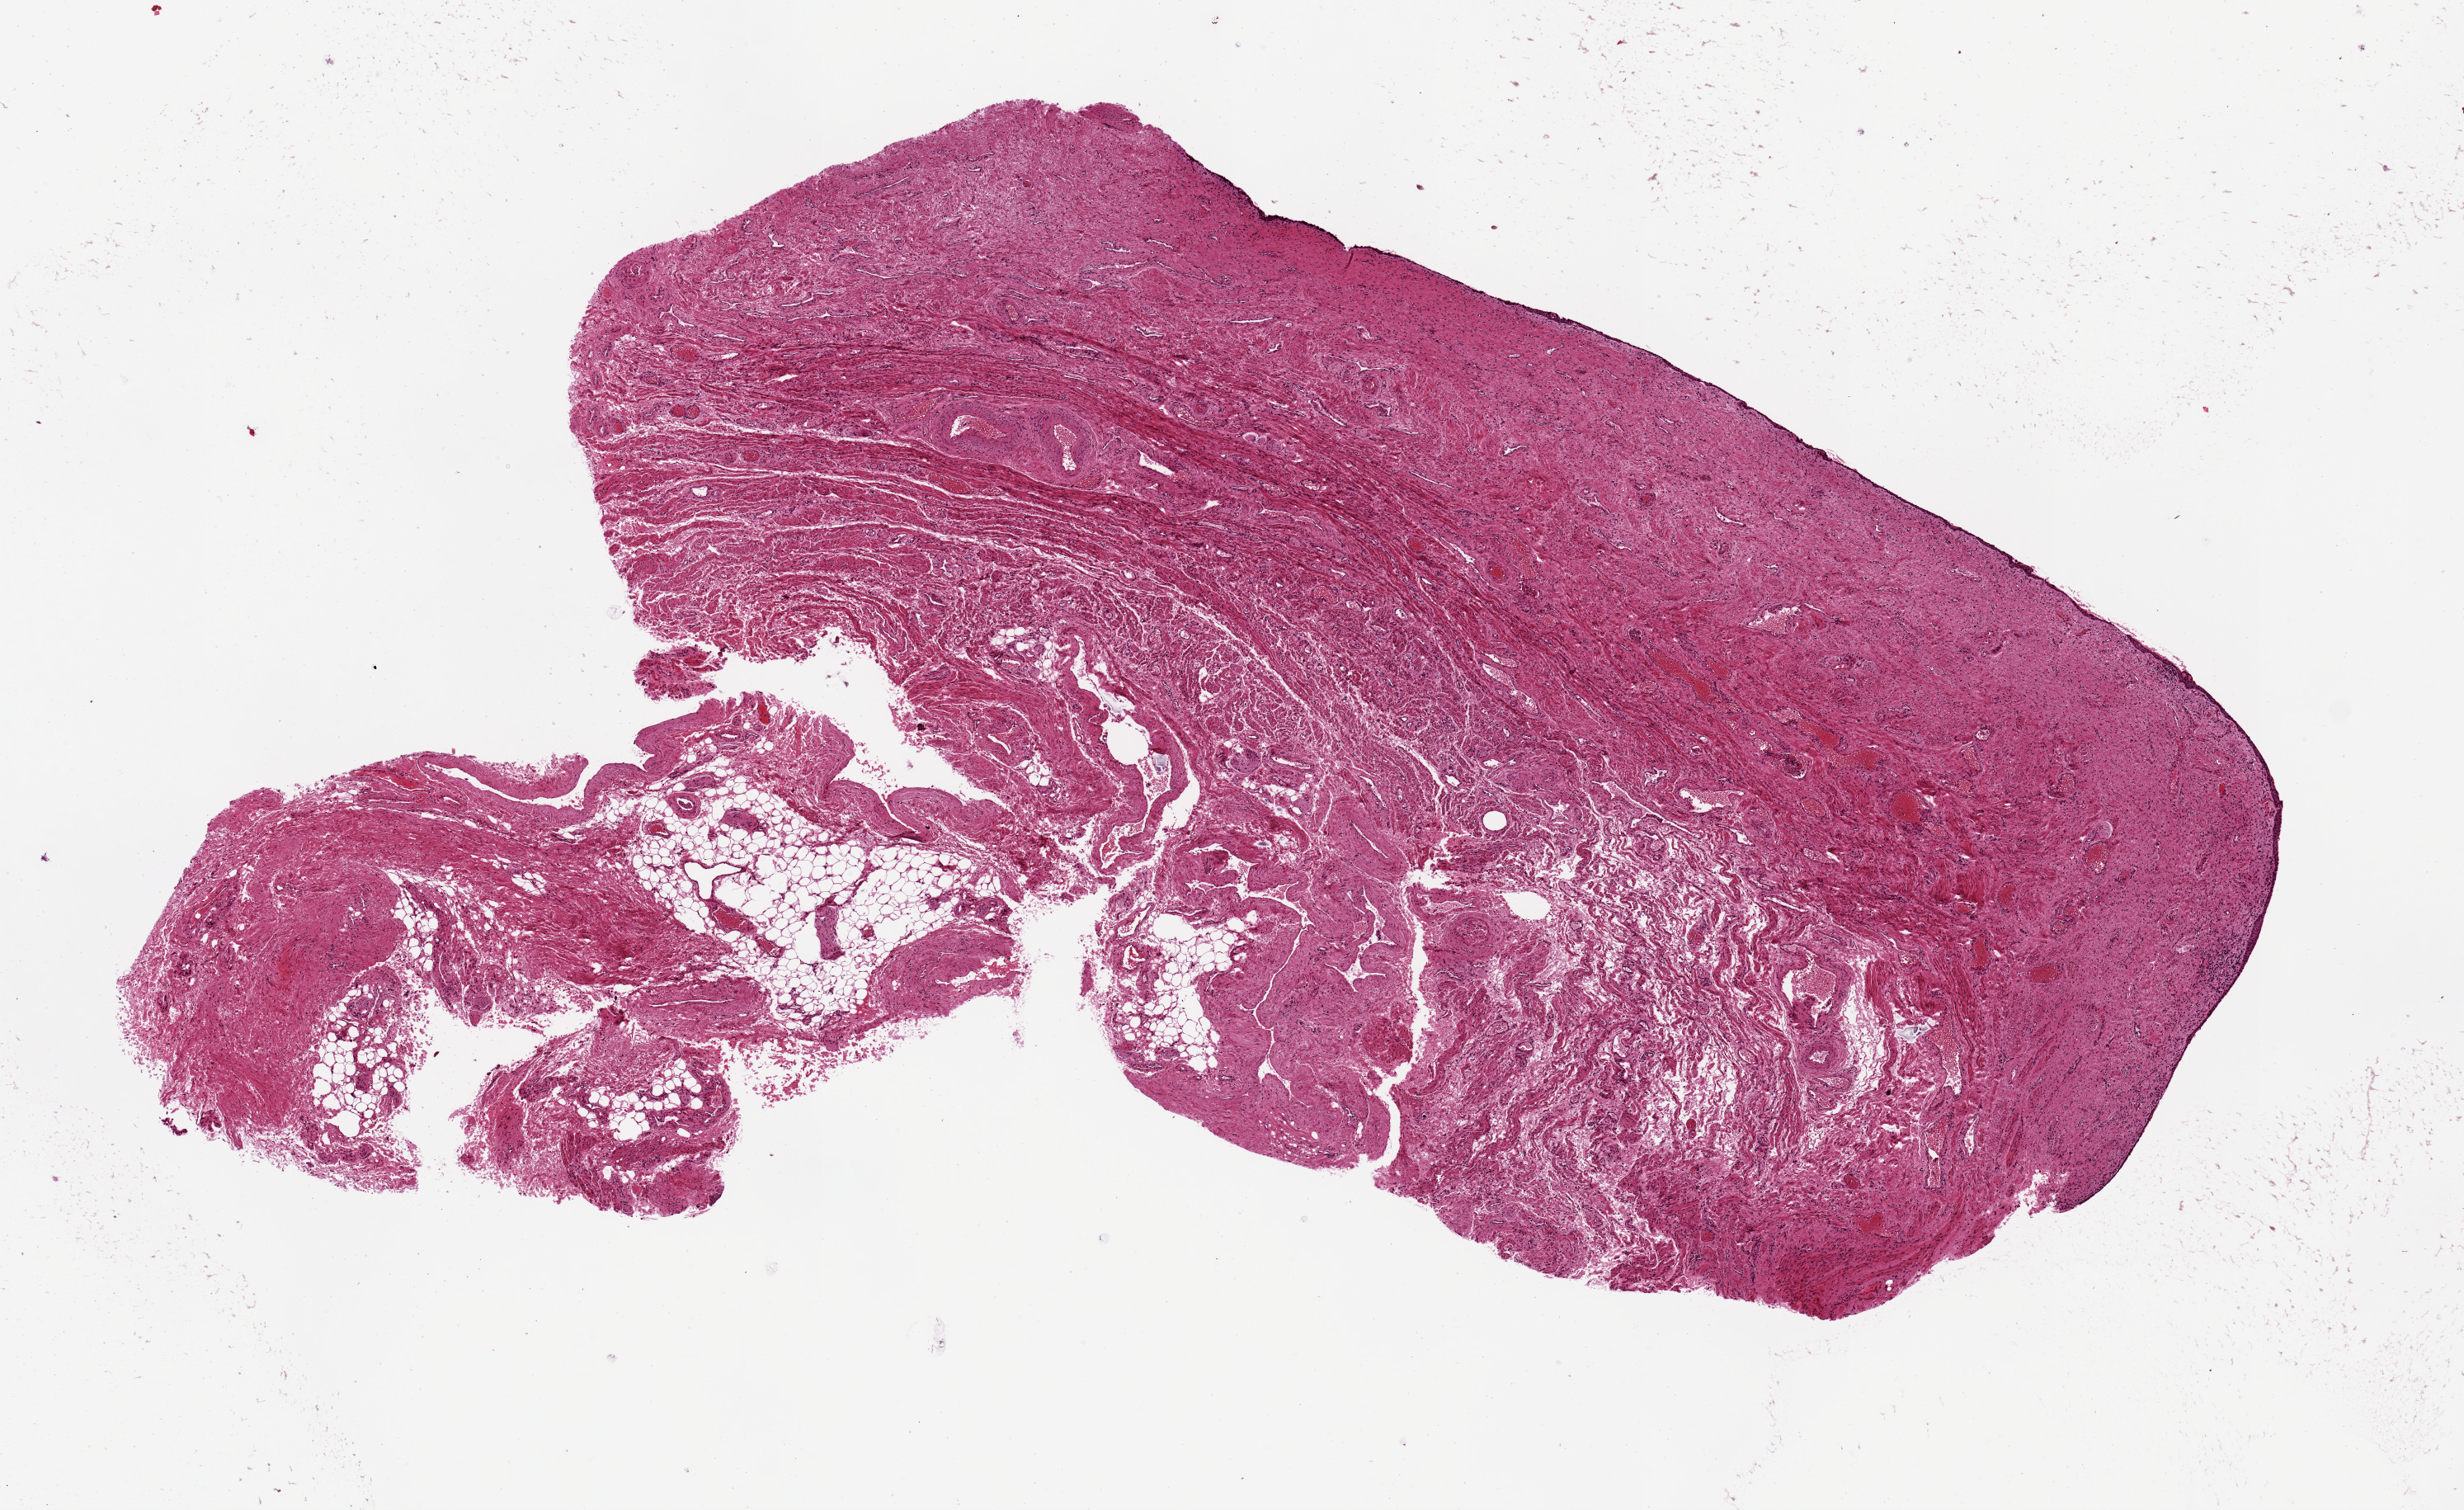
Whole-slide image, haematoxylin and eosin stain, whole scanned area (about 11.8 x 7.2 mm, slide scanned at 20x) shown as a low-resolution overview; PAXgene-fixed, paraffin-embedded tissue; section of vagina (target tissue); donor tissue sample.
Reviewer comment on this tissue sample: Largely denuded epithelium less than 0.1% of total thickness.